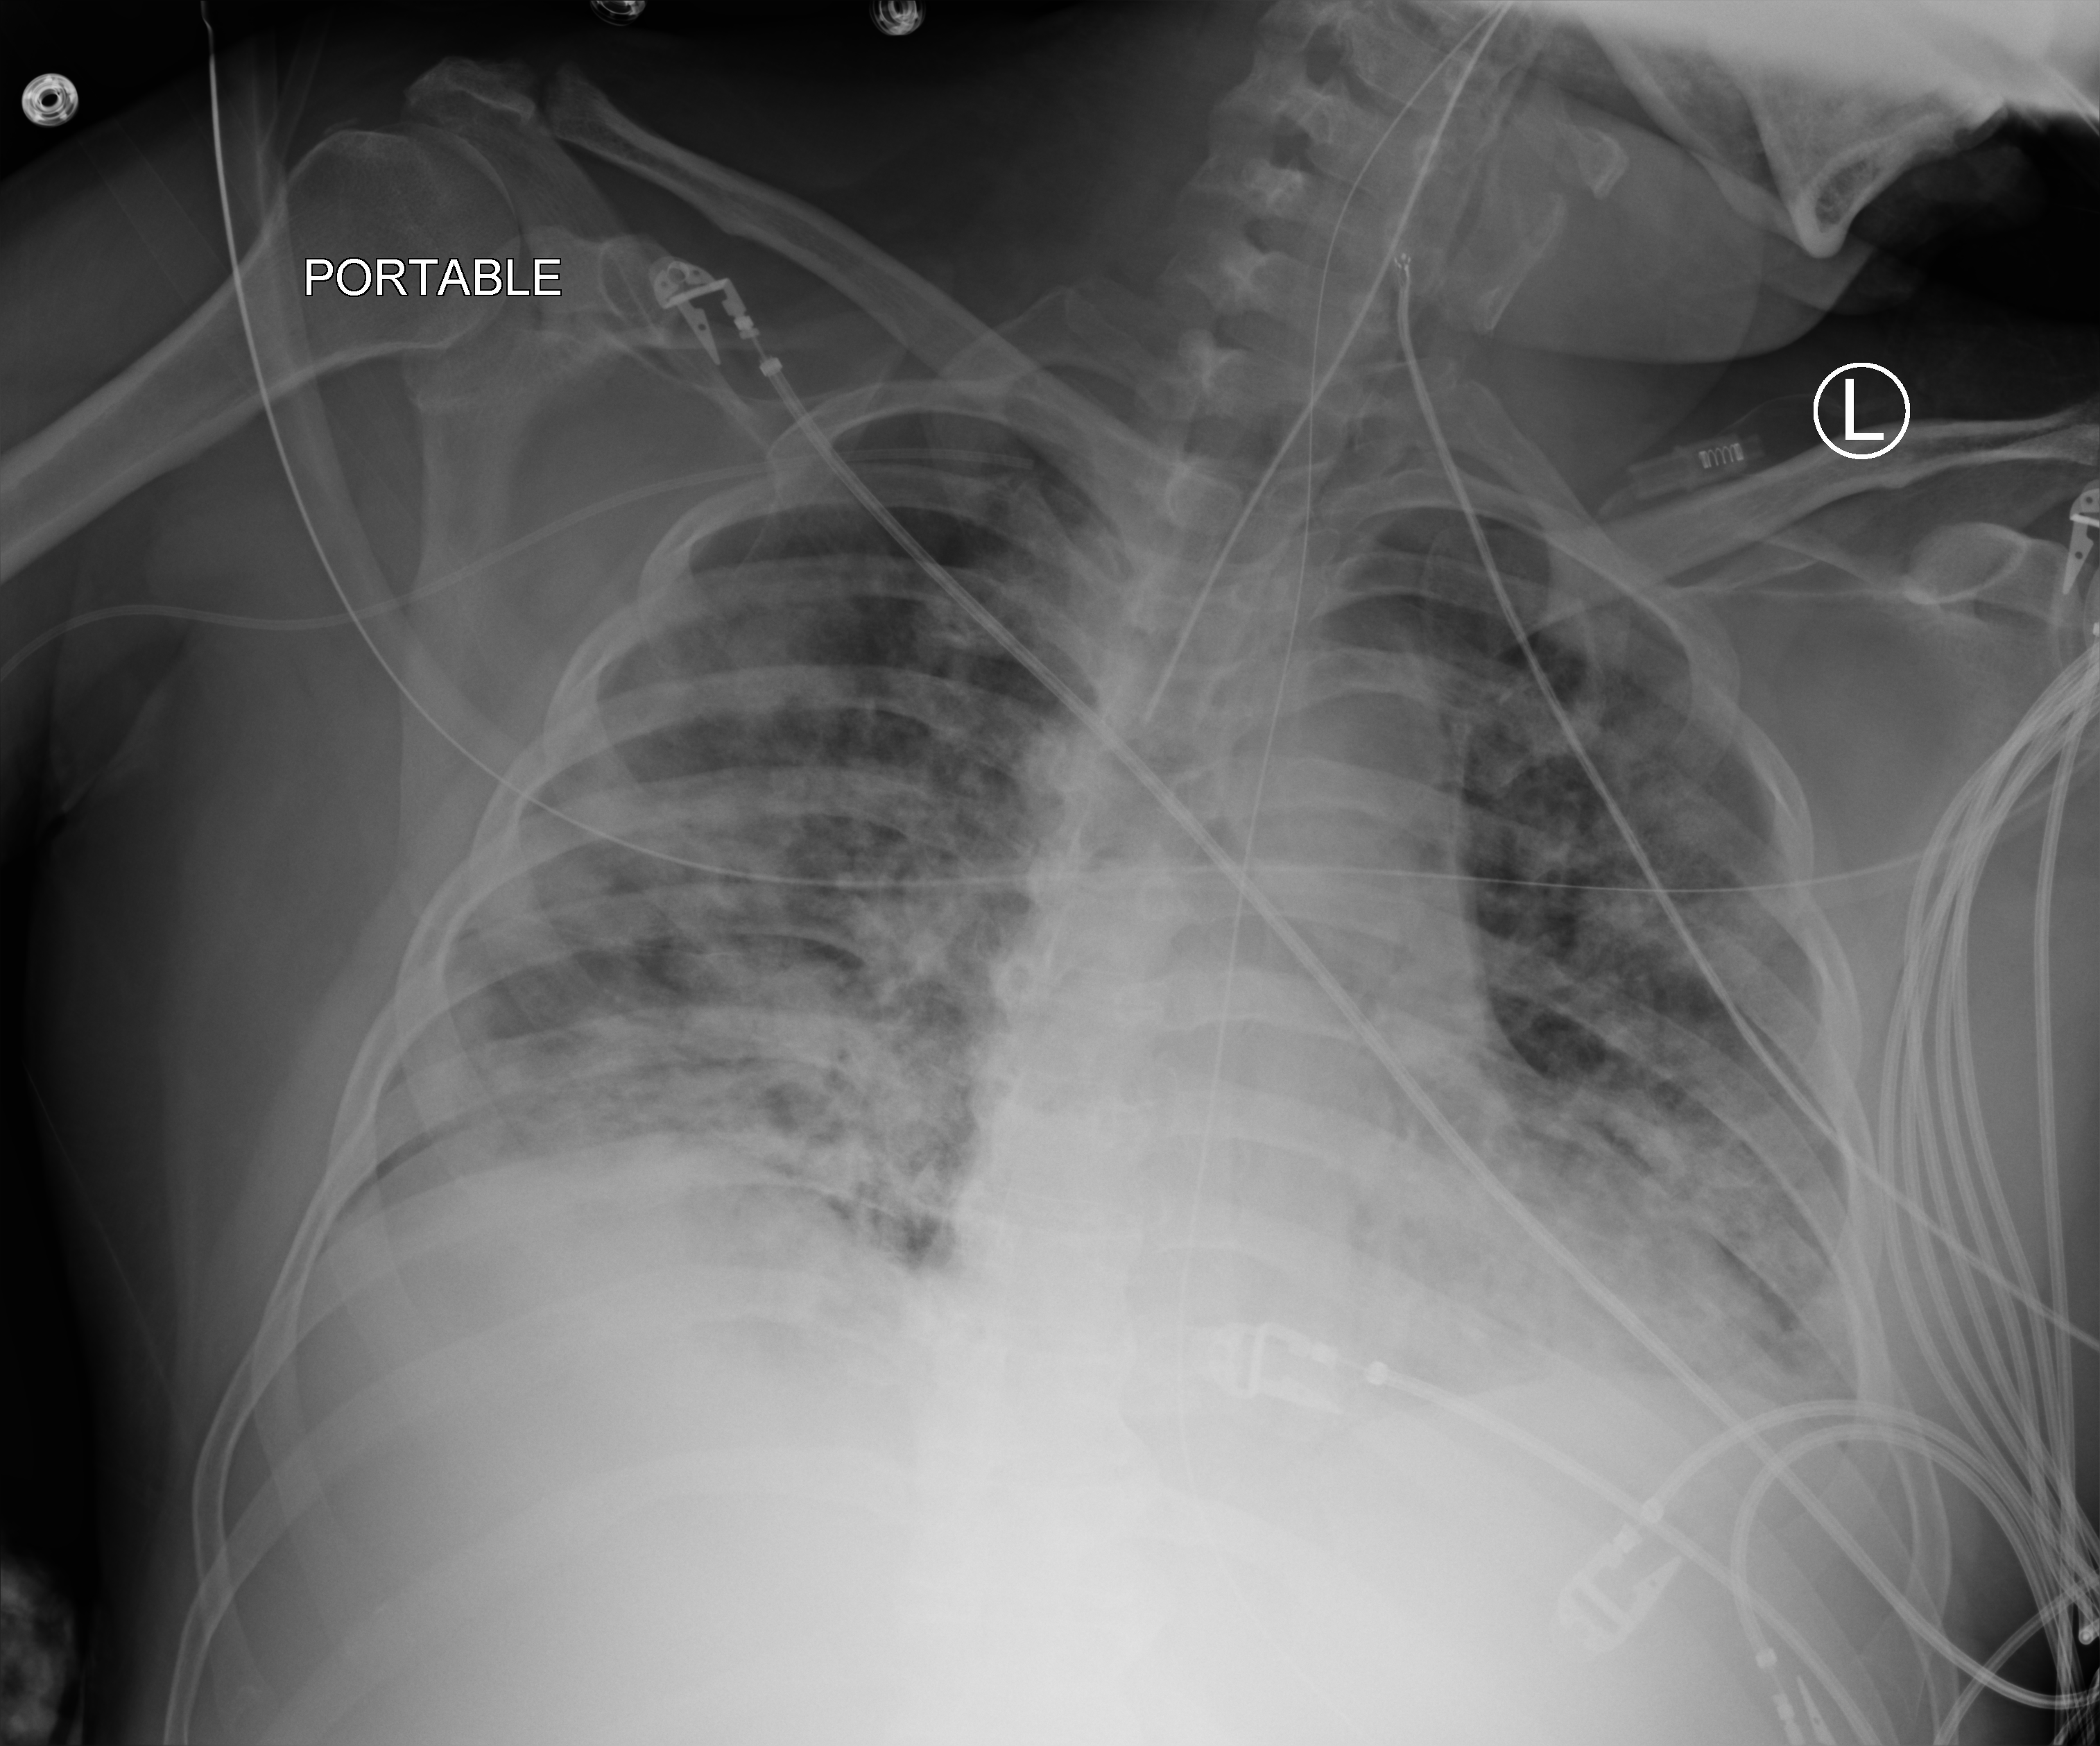
Portable chest radiograph; anteroposterior (AP) projection. Patient hospitalised with COVID-19; male, aged 18–59 years.
Hospital-stay facts (about this admission, not read from this image; timing relative to this image not recorded): mechanically ventilated during this hospital stay: yes; admitted to intensive care during this hospital stay: yes; diabetes (admission record): yes.